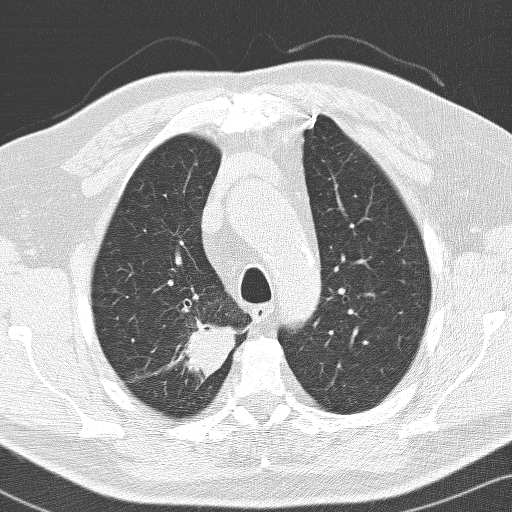
Low-dose screening chest CT, one axial slice; position 111 of 141 along the scan axis; lung window (W 1500 / L -600 HU); 3.2 mm slice thickness; 512 × 512 image matrix, field of view 326 × 326 mm.
Annotated regions visible in this slice (outlined manually by an expert reader):
- lesion 1 (tumor, upper lobe of right lung): bounding box <179,318,240,378> (left, top, right, bottom; pixels)